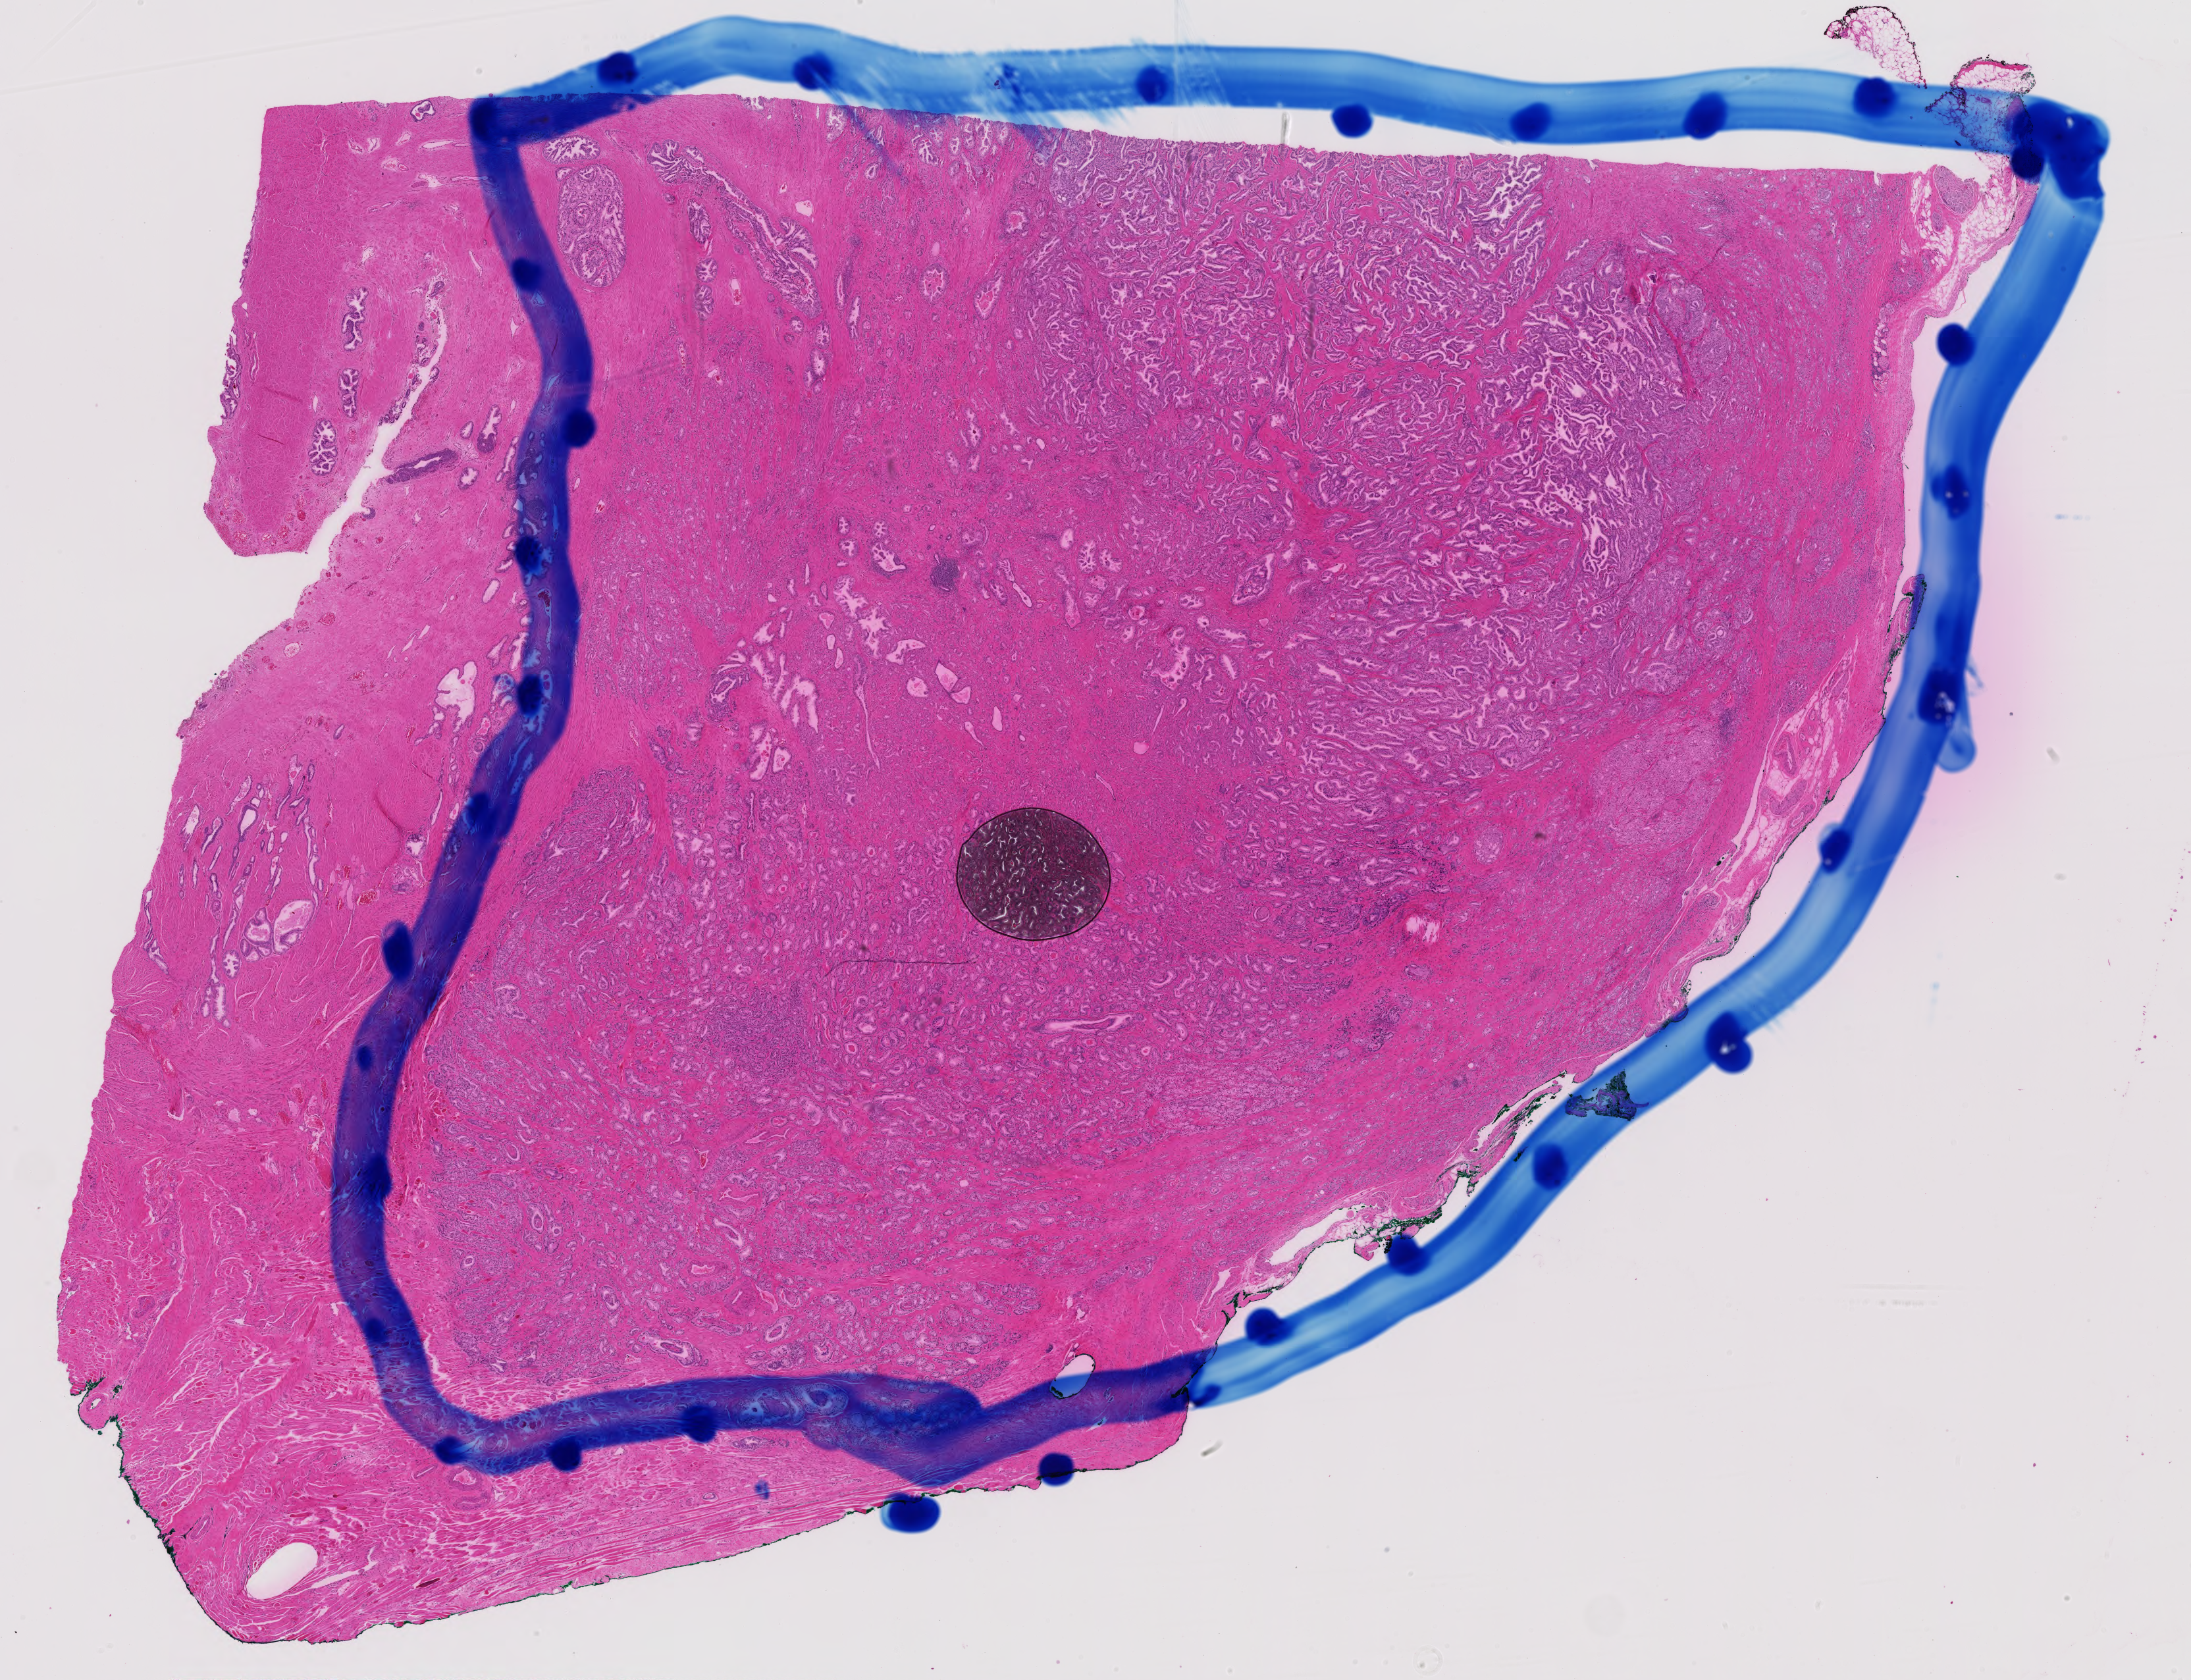
Digitized Hematoxylin and eosin (H&E) stained tissue section (whole slide), shown as a low-resolution overview of the whole scanned area (about 24.1 x 18.5 mm, slide scanned at 40x). Formalin-fixed paraffin-embedded (FFPE) diagnostic section. Prostate, primary tumour sample. Male, age 69 years at initial diagnosis. Gleason score: 7 (4+3).
Pathologic diagnosis: Adenocarcinoma, NOS (prostate gland).